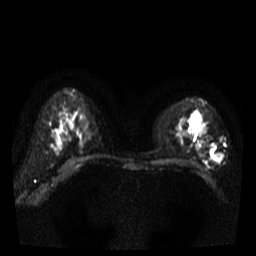
Breast MRI, one axial slice; position 26 of 38 along the scan axis; diffusion-weighted series; image 2 of 4 stored at this slice position (different b-values; order by instance number); 3 T; 5 mm slice thickness; 256 × 256 image matrix, field of view 320 × 320 mm. Female patient.
Structures marked on this image (manually delineated by an expert):
- tumour on diffusion-weighted imaging: bounding box [x1, y1, x2, y2] px = [214, 154, 223, 162]